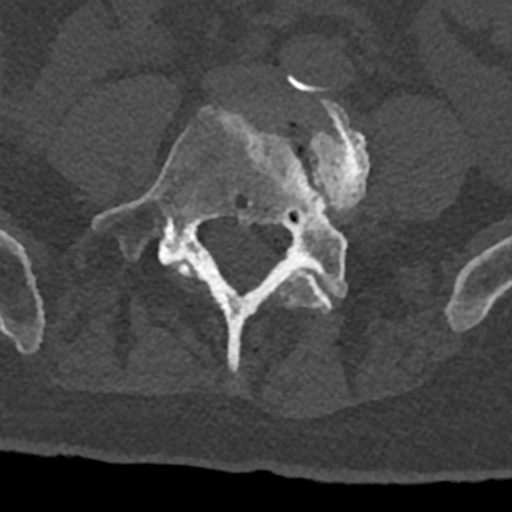
CT including the spine, one axial slice; slice 216 of 797 in the series (ordered by position); 120 kVp; bone window (W 1800 / L 400 HU); 512 × 512 image matrix, field of view 160 × 160 mm. Male patient, age 74 years. Case-level facts recorded for this patient, not image findings: primary cancer: renal; vertebrae with lytic lesions (as recorded): T10, L1, L2, L3, L4, L5.
Annotated regions visible in this slice (semi-automatic segmentation, software-assisted and operator-edited):
- L4 vertebra: bounding box (x1, y1, x2, y2) in pixels: (174, 89, 370, 315)
- L5 vertebra: (92, 106, 347, 372)